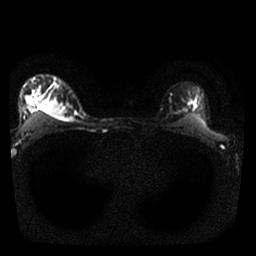
Breast MRI, one axial slice. Position 24 of 25 along the scan axis. Diffusion-weighted series; image 2 of 4 stored at this slice position (different b-values; order by instance number). 1.5 T. 4 mm slice thickness. 256 × 256 image matrix, field of view 310 × 310 mm. Female patient.
Outlined on this slice (expert manual segmentation):
- tumour on diffusion-weighted imaging: bounding box <42,99,63,117> (left, top, right, bottom; pixels)